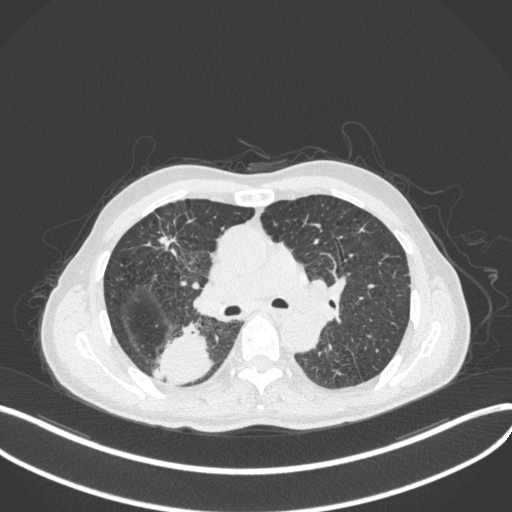
Chest CT, one axial slice. Slice 276 of 423 in the series (ordered by position). Reconstruction kernel B31f. Lung window (W 1500 / L -600 HU). 1 mm slice thickness. 512 × 512 image matrix, field of view 400 × 400 mm. Male patient, age 79 years. From the clinical record (not read from this slice): clinical TNM (as recorded): T3 N0 M0.
Outlined on this slice (rectangle marked by the reading radiologist):
- lung tumour (recorded histology: adenocarcinoma): box from (x=151, y=316) to (x=216, y=387) px